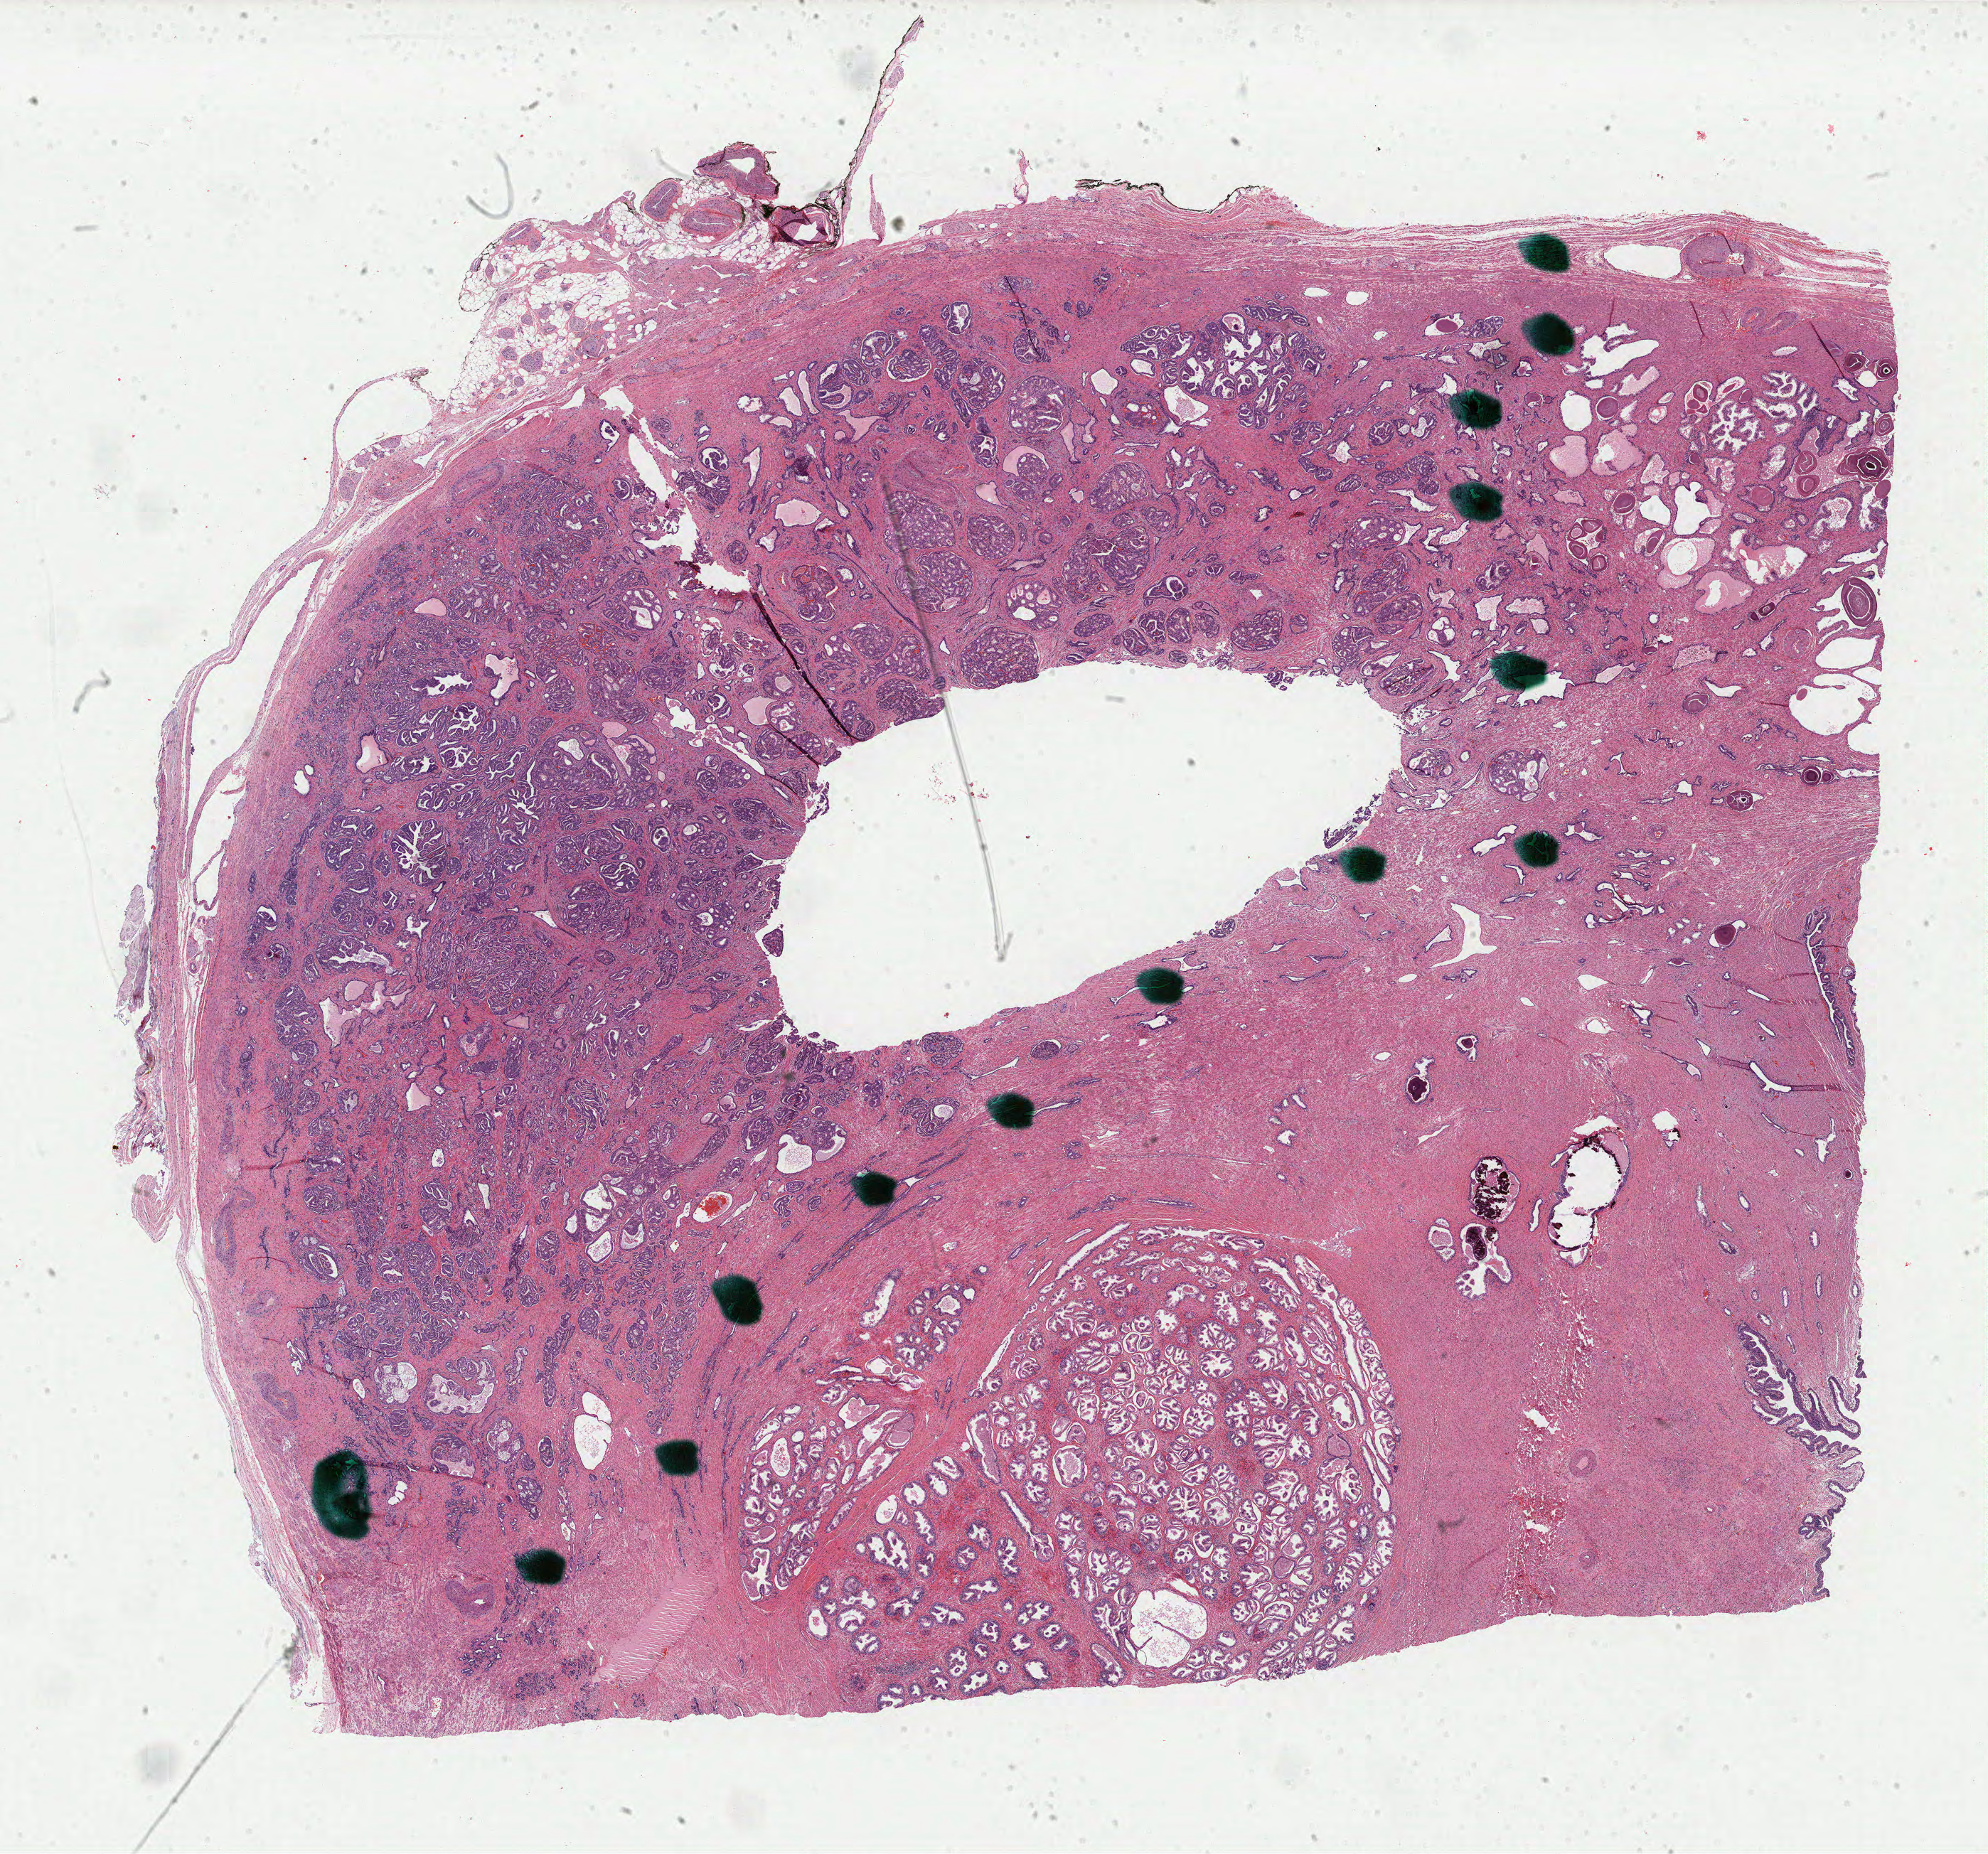
Digitized H&E tissue section (whole slide), shown as a low-resolution overview of the whole scanned area (about 22.2 x 20.7 mm, from a 40x scan), FFPE section, sample: primary tumour, prostate. Male patient; age at initial diagnosis 65 years. Gleason score: 7 (4+3).
- laterality: bilateral
- pathologic diagnosis: Adenocarcinoma, NOS (prostate gland)